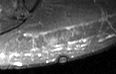
MRI of an extremity soft-tissue mass, one axial slice; STIR; MR volume resampled by the dataset authors to the PET/CT grid (not the native acquisition matrix); 116 × 74 image matrix, field of view 113 × 72 mm. Male patient. From the clinical record (not read from this slice): histological type: pleiomorphic leiomyosarcoma; grade: high; site of the primary tumour: left buttock.
Annotated regions visible in this slice (expert contour drawn on MRI and transferred to this co-registered scan by the dataset authors):
- gross tumour volume including surrounding oedema: bounding box <60,28,70,43> (left, top, right, bottom; pixels)
- gross tumour volume (mass): <62,33,69,43>